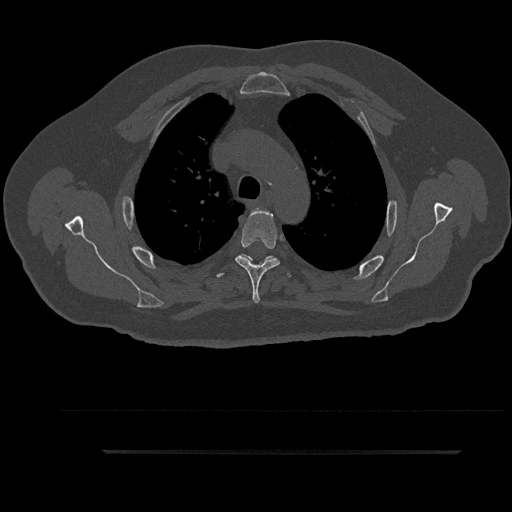
CT including the spine, one axial slice; position 668 of 797 along the scan axis; reconstruction kernel Br40s/3; 120 kVp; bone window (W 1800 / L 400 HU); 0.5 mm slice thickness; 512 × 512 image matrix, field of view 432 × 432 mm. Male patient, age 63 years. From the clinical record (not read from this slice): primary cancer: renal.
Structures marked on this image (semi-automatically segmented with operator editing):
- T4 vertebra: bounding box [x1, y1, x2, y2] px = [235, 209, 280, 303]
- T5 vertebra: [257, 258, 268, 266]